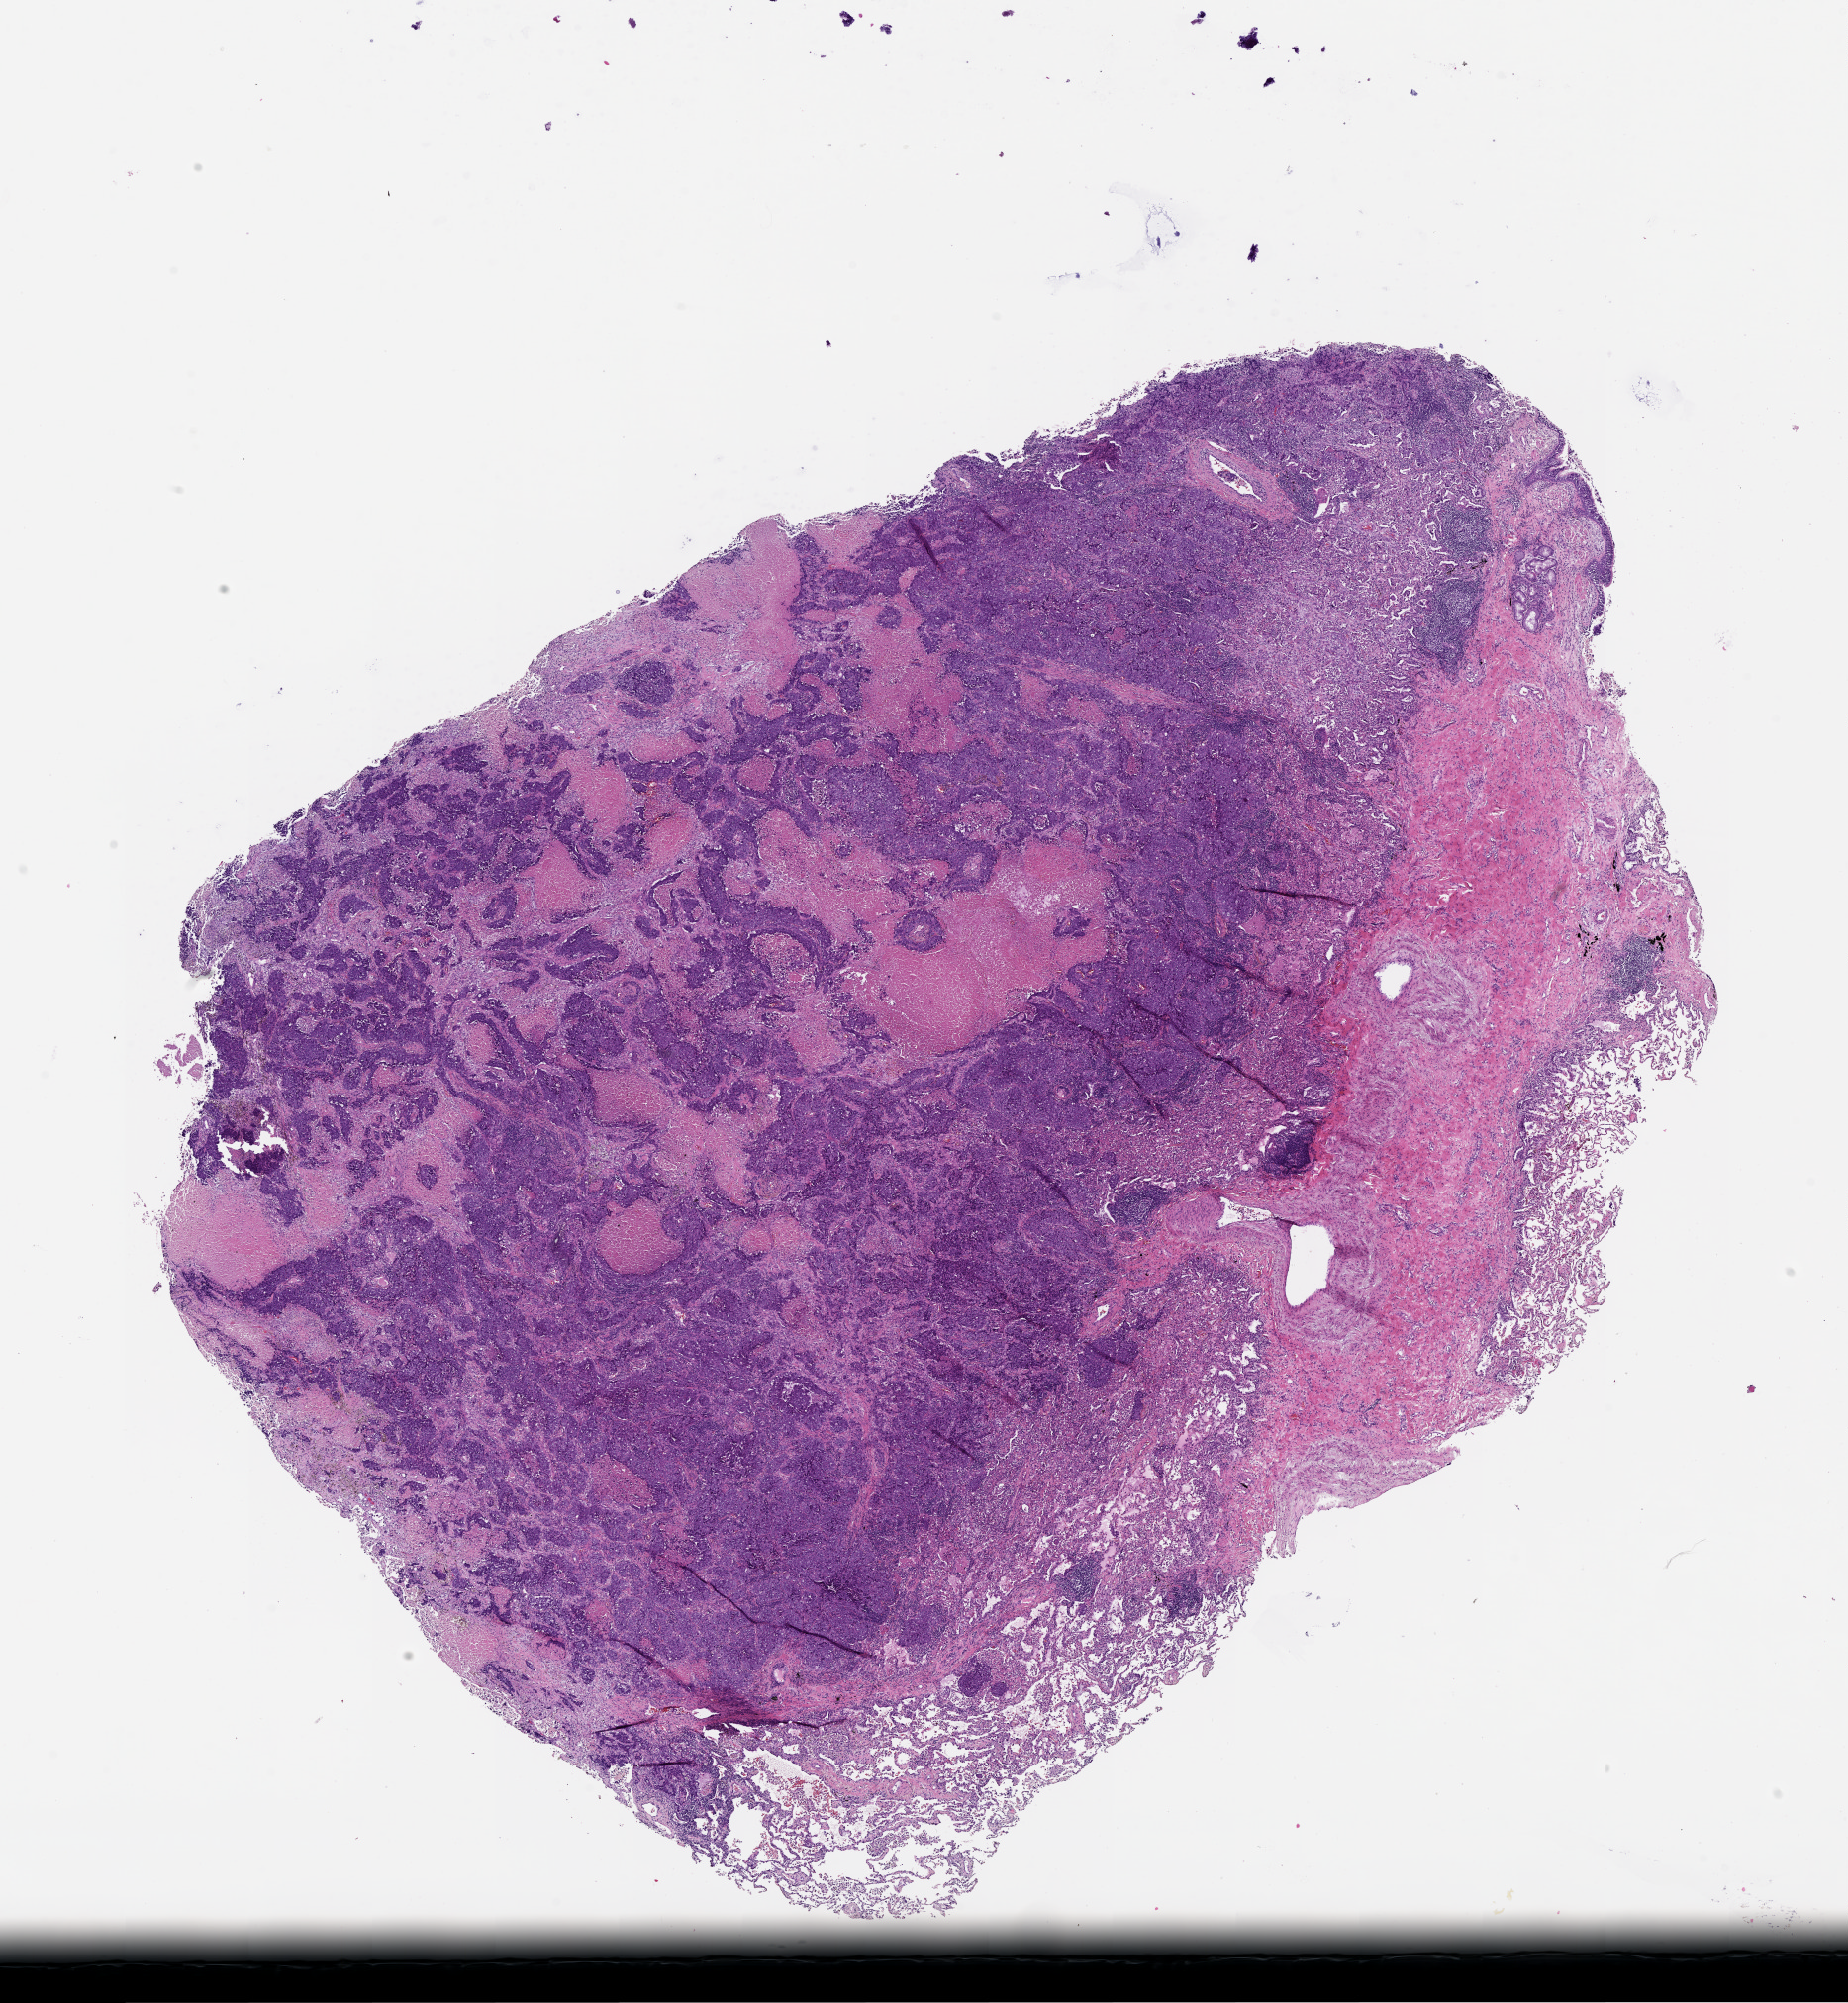
Whole-slide histology image, H&E-stained — whole scanned area (about 15.0 x 16.3 mm) shown as a low-resolution overview; lung, tumour tissue. 60-year-old male patient.
Patient diagnosis (cohort enrolment): squamous cell carcinoma (lung).